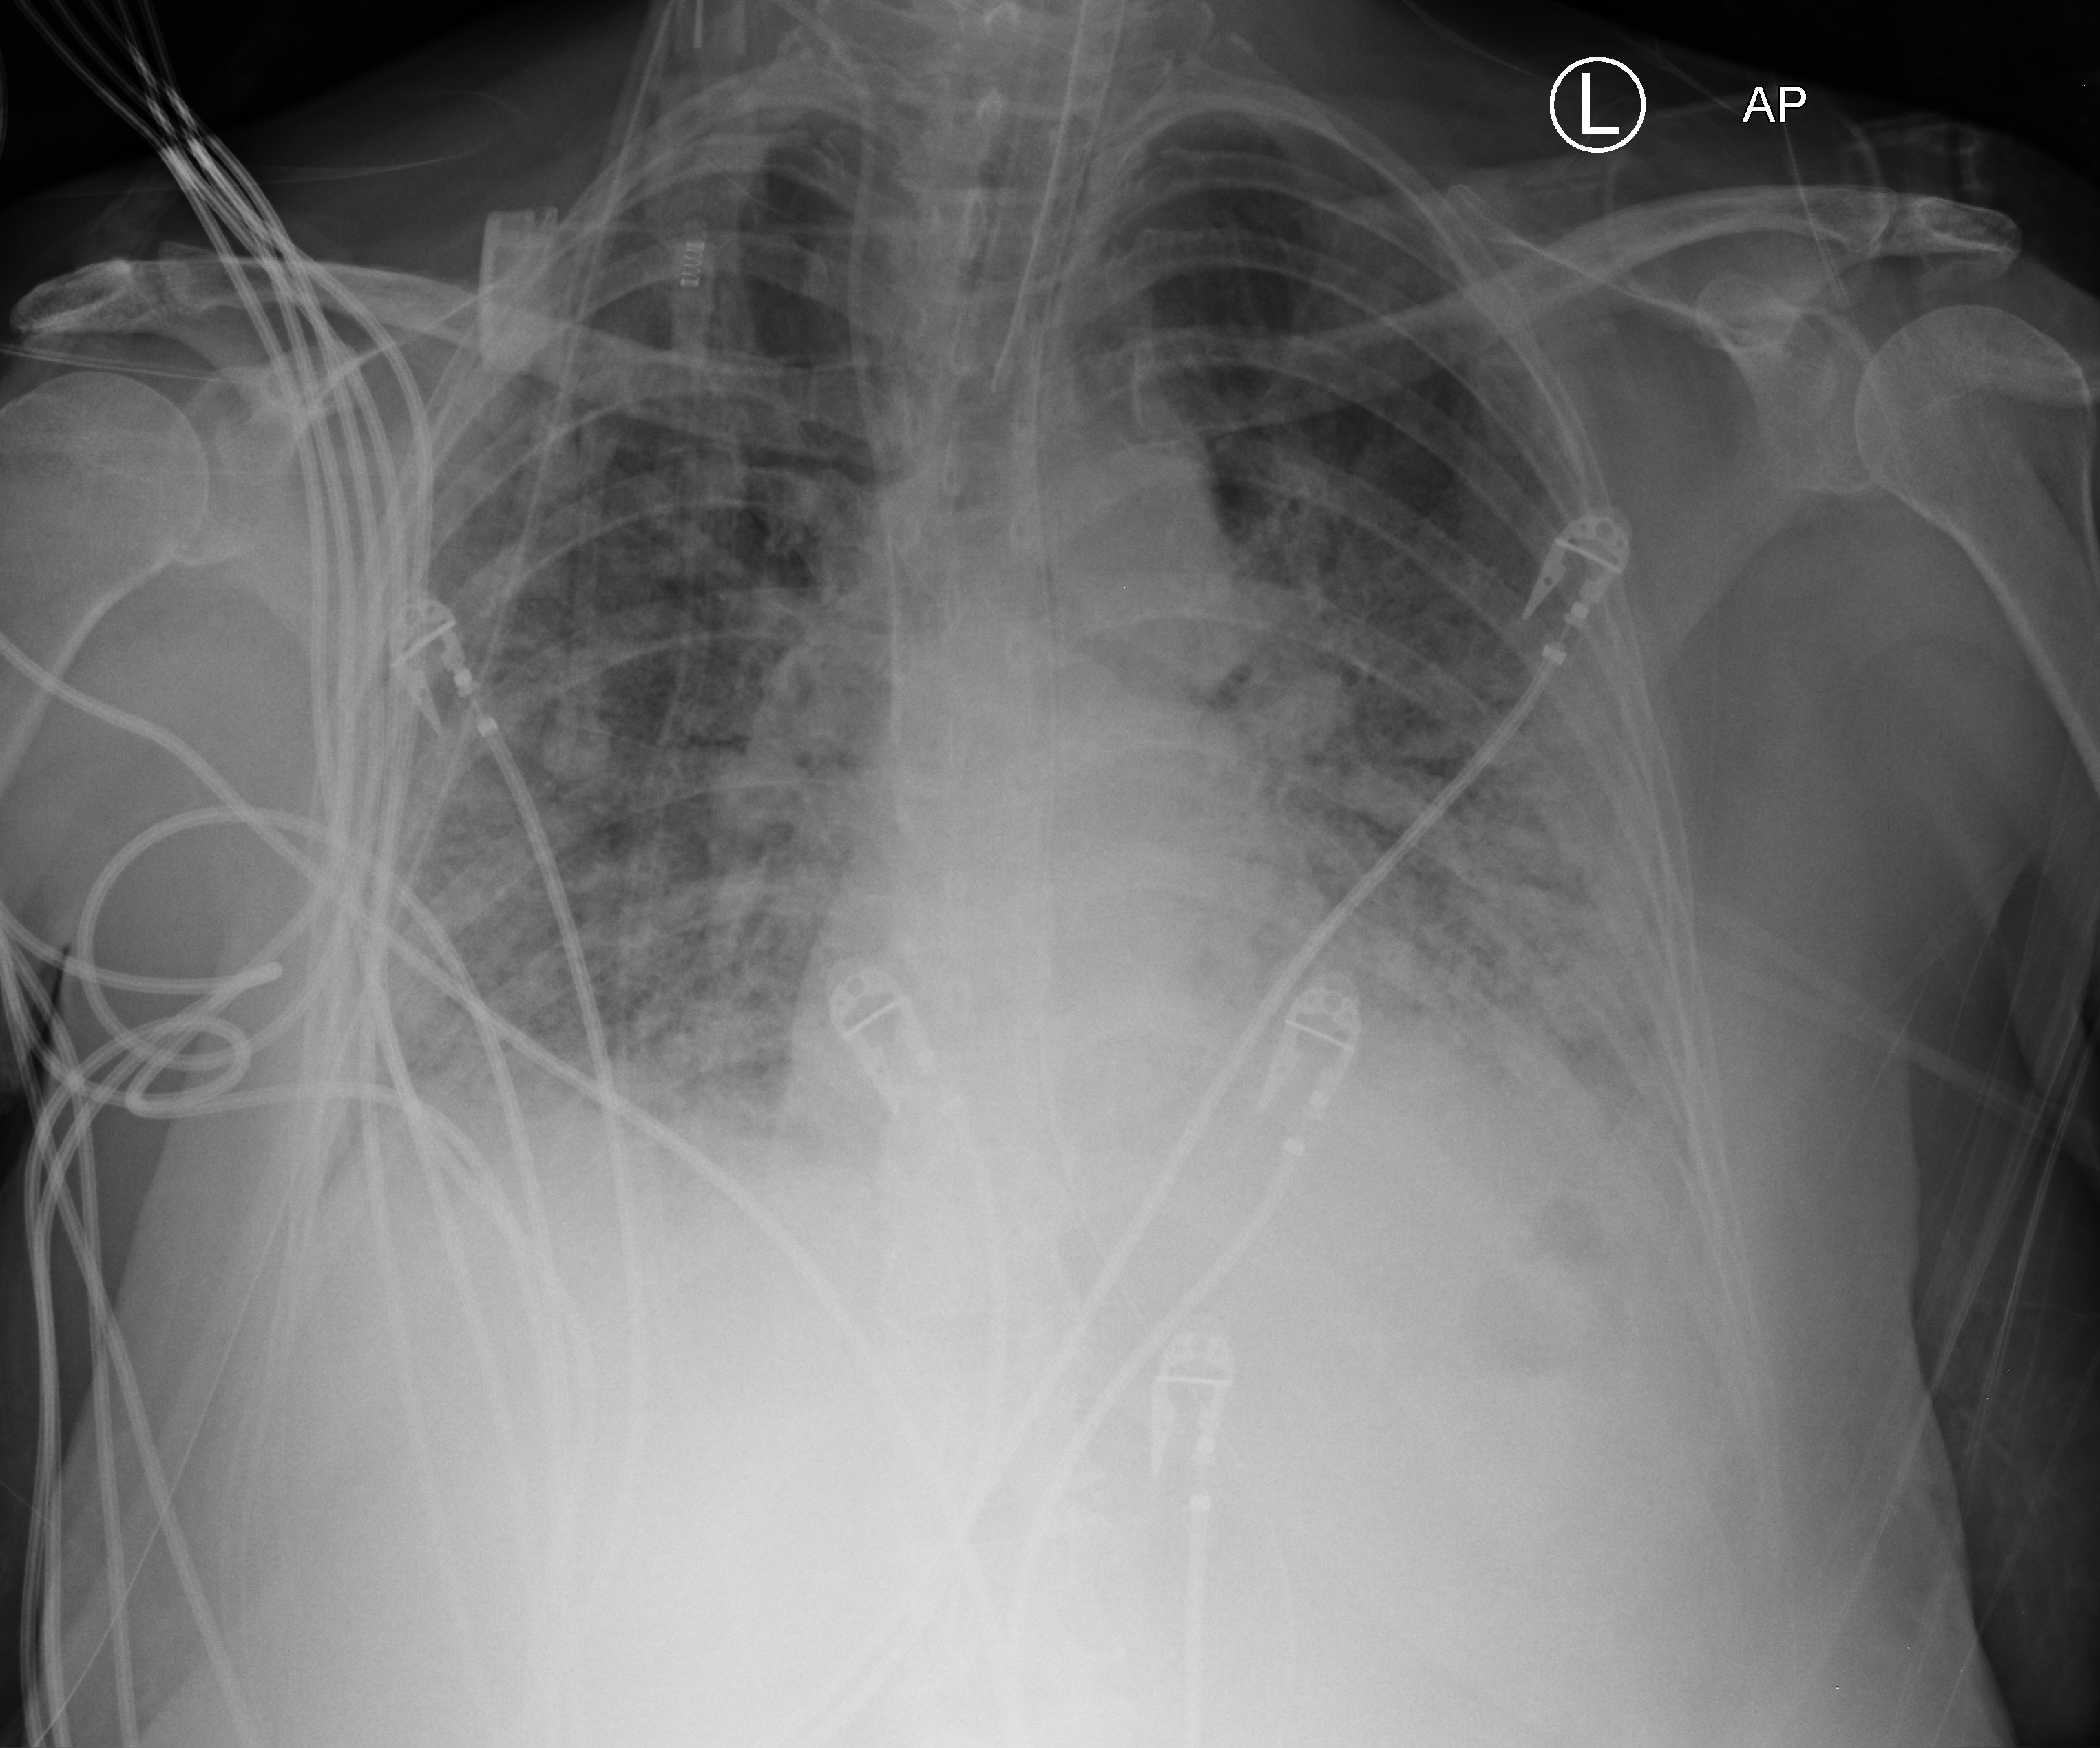
Portable chest radiograph, anteroposterior (AP) projection. Patient hospitalised with COVID-19; female, aged 60–74 years.
Hospital-stay facts (about this admission, not read from this image; timing relative to this image not recorded): admitted to intensive care during this hospital stay: yes.